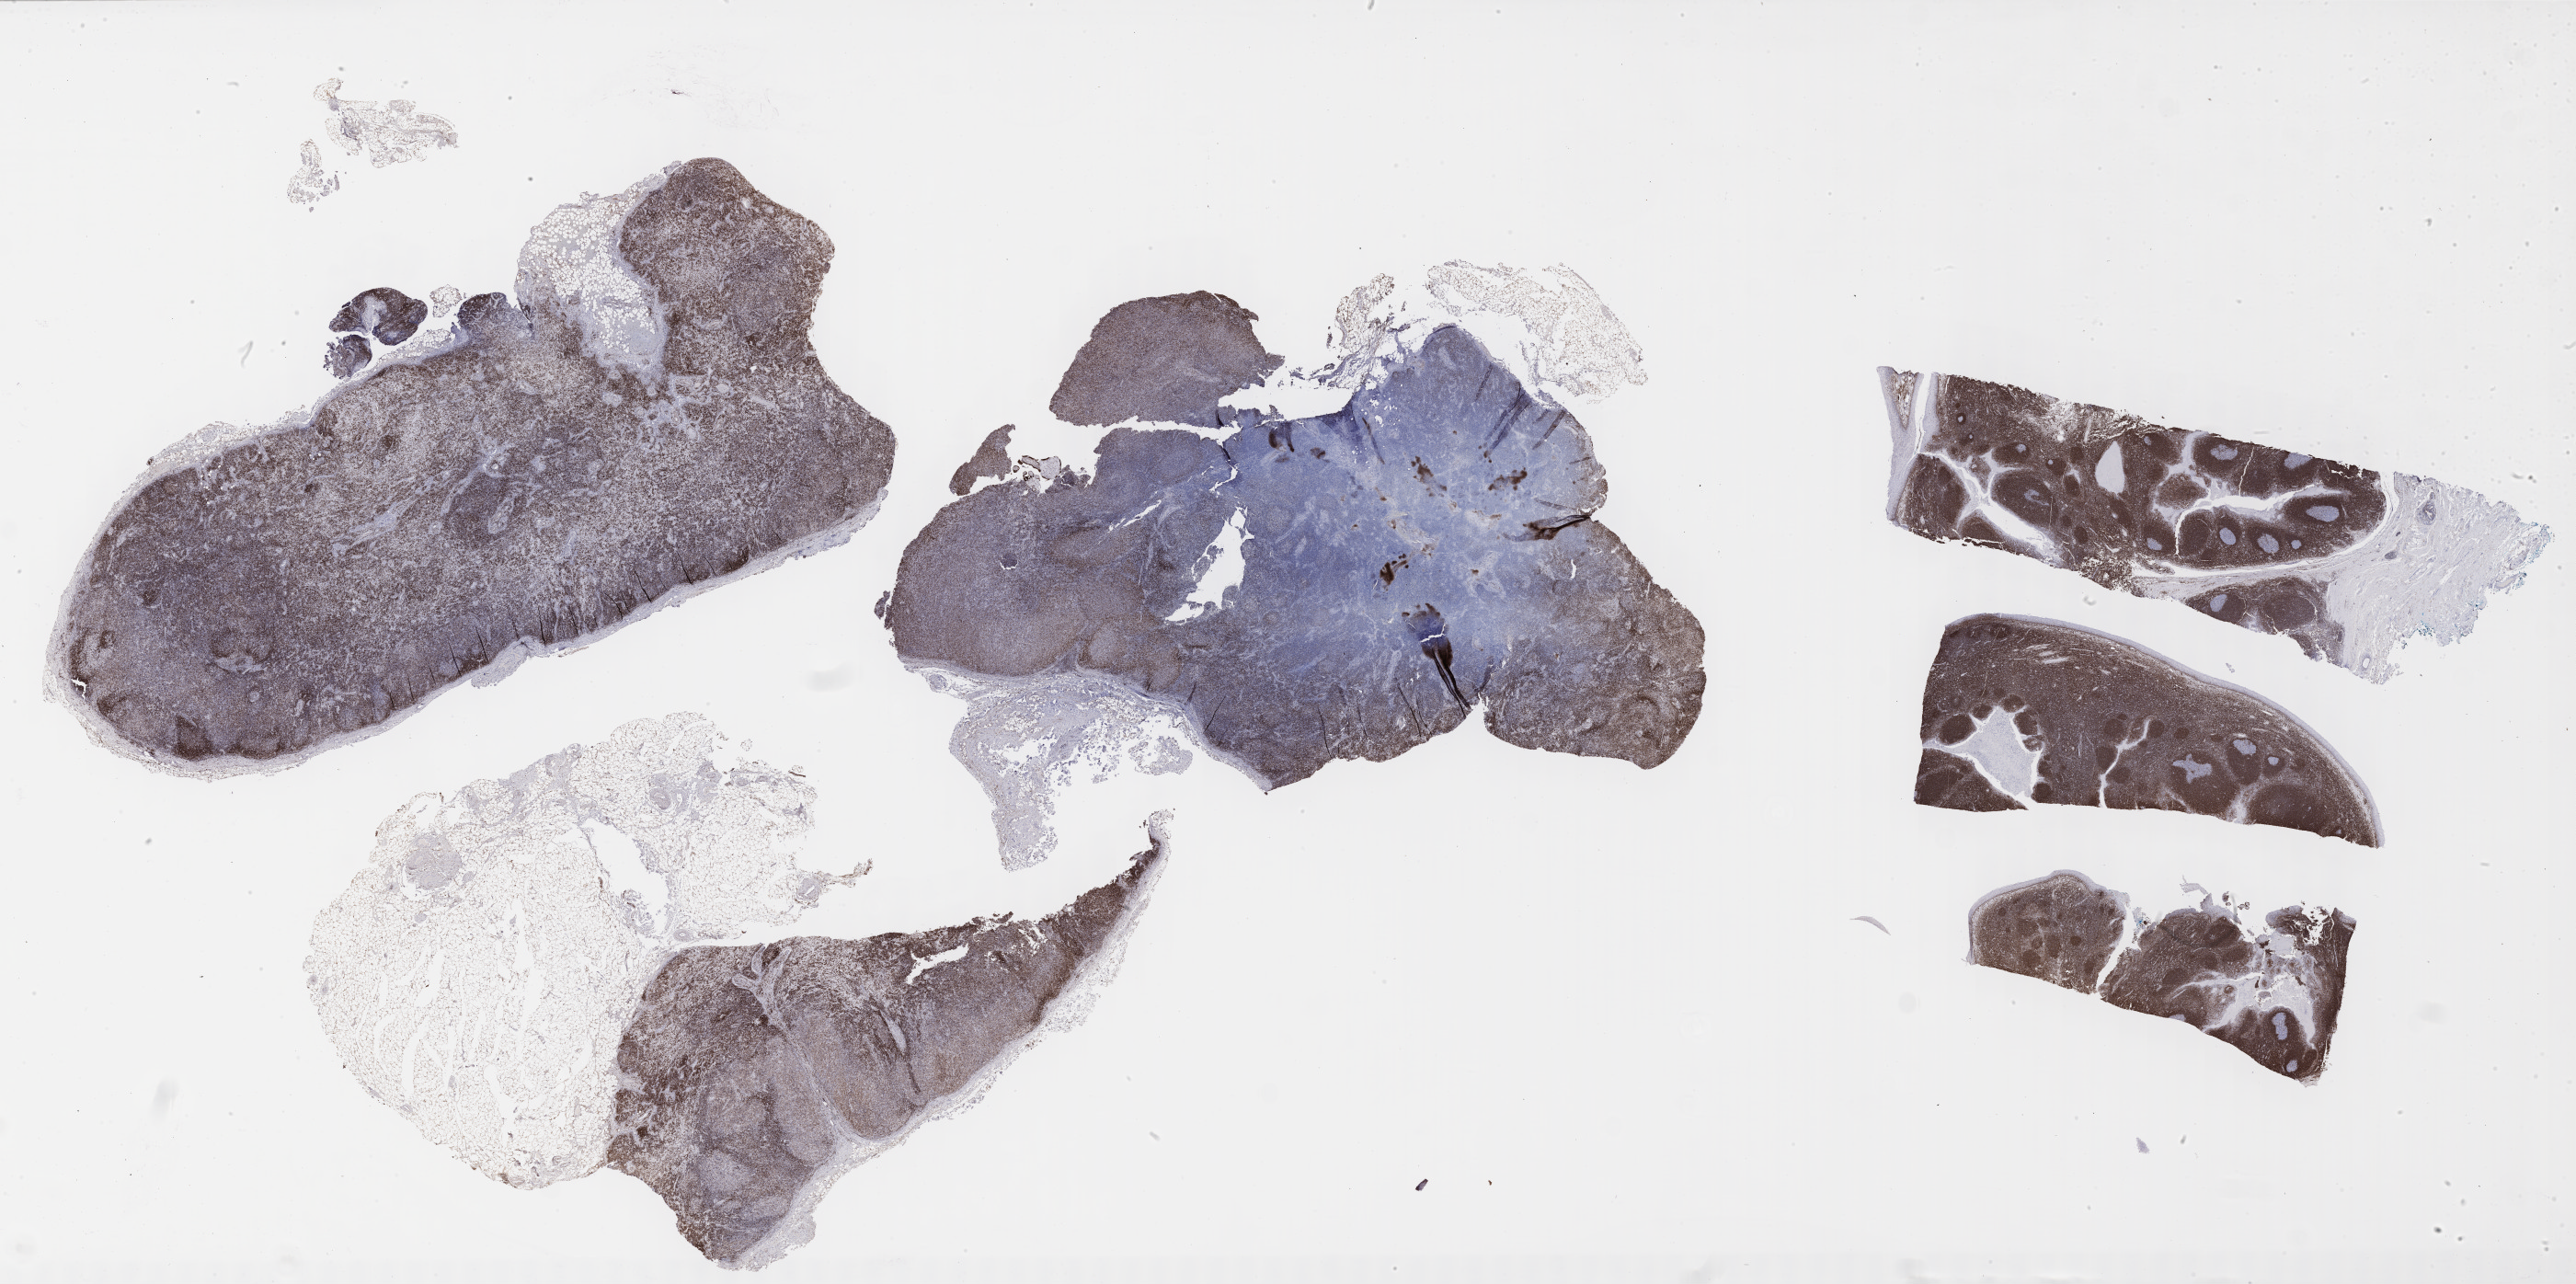
Immunohistochemistry (IHC) whole-slide image stained for BCL2 — whole scanned area (about 45.3 x 22.6 mm) shown as a low-resolution overview. Specimen: tumor tissue. Site: lymph node. Male patient, aged 56.
Histologic diagnosis: Diffuse large B-cell lymphoma, NOS.